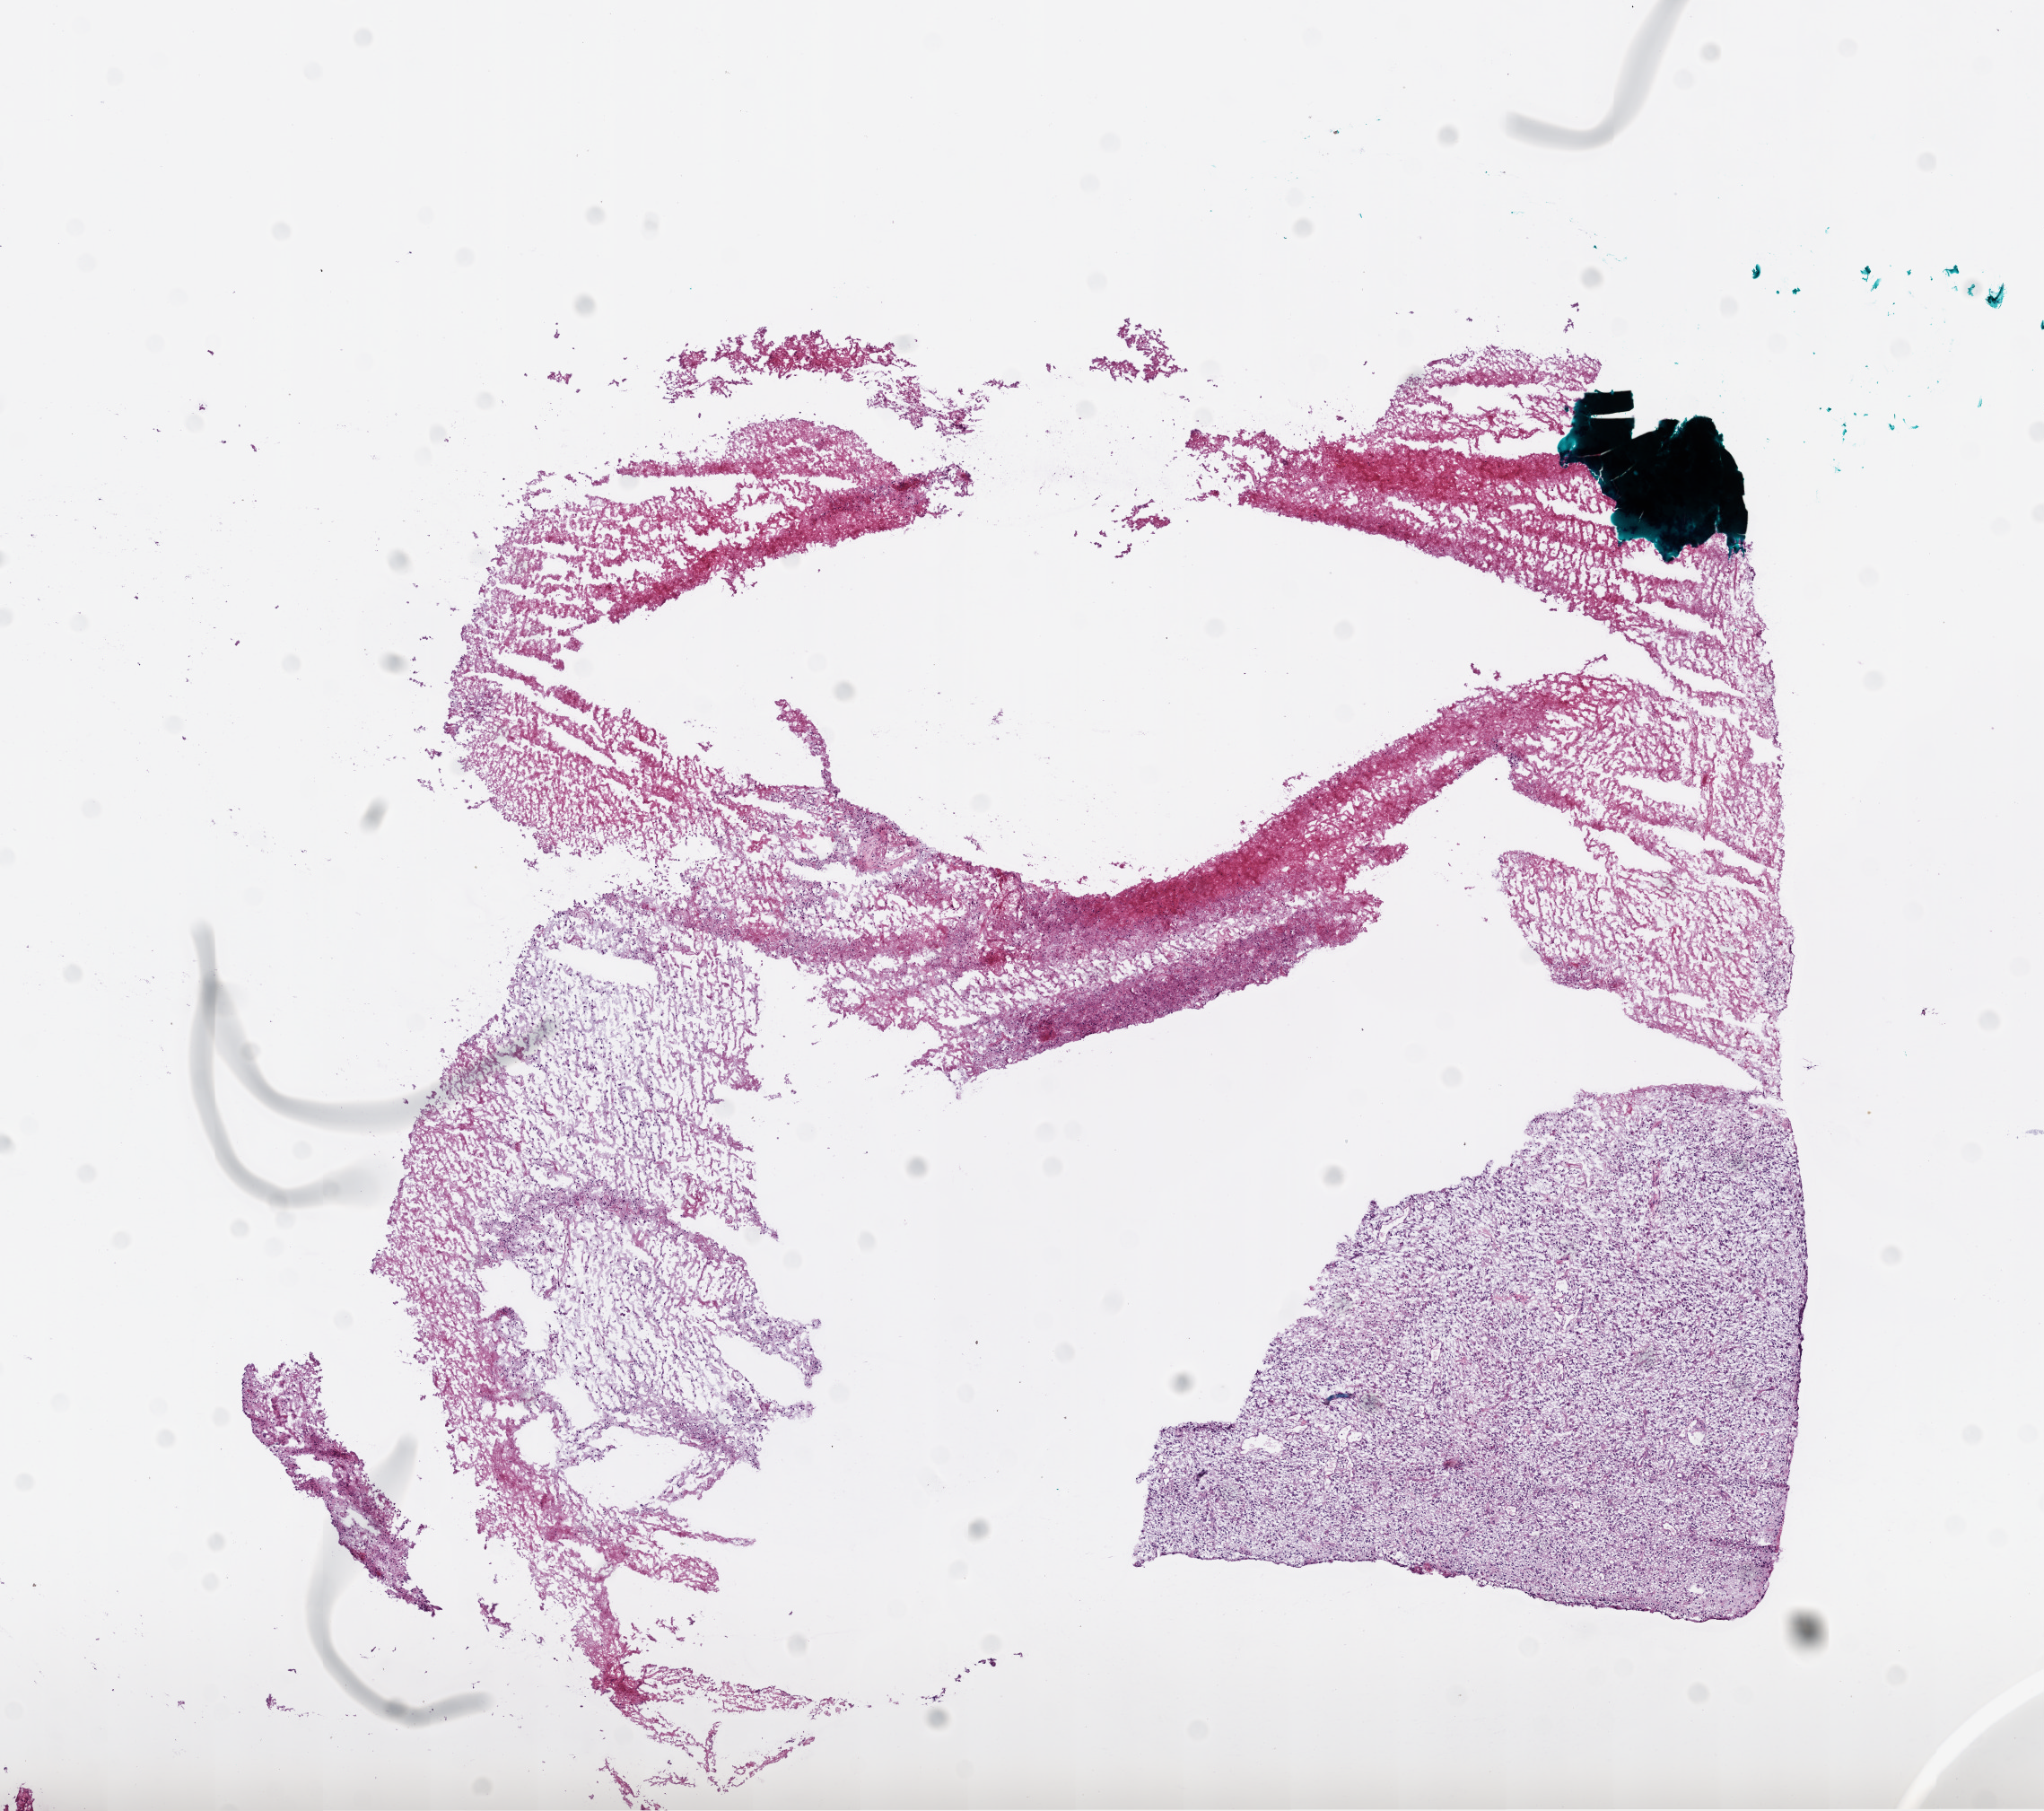
Digitized H&E-stained tissue section (whole slide), shown as a low-resolution overview of the whole scanned area (about 9.2 x 8.1 mm), frozen section from the bottom of the tissue portion, brain, primary tumour sample. Male, age 56 years at initial diagnosis. Composition of this section per pathologist review: tumour cells 60%, tumour nuclei 90%, stromal cells 10%, necrosis 30%.
Histologic diagnosis: Glioblastoma.